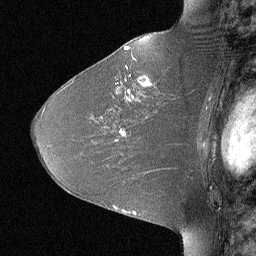
Breast MRI (dynamic contrast-enhanced), one sagittal slice; position 42 of 64 along the scan axis; dynamic contrast-enhanced study with each time point stored as its own series, time point 2 of 3 at this slice position (early post-contrast, ordered by acquisition time); 1.5 T; TE 4 ms, TR 30 ms; 2.25 mm slice thickness; 256 × 256 image matrix, field of view 180 × 180 mm. Patient: female, 46 years. Case-level facts recorded for this patient, not image findings: setting: breast cancer imaged before/during neoadjuvant chemotherapy; receptor status: HR-positive, HER2-negative.
Annotated regions visible in this slice (semi-automatically segmented with operator editing):
- analysis volume of interest (the breast-tissue region the enhancement analysis was run in; not a lesion): bounding box <106,43,184,119> (left, top, right, bottom; pixels)
- tumour enhancement mask (voxels above the 90 % enhancement threshold inside the analysis volume of interest): <124,47,148,93>